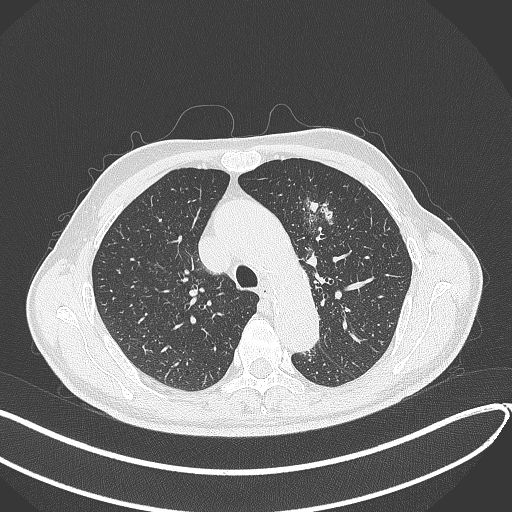
Chest CT, one axial slice. Reconstruction kernel B70f. 120 kVp. Lung window (W 1500 / L -600 HU). 512 × 512 image matrix, field of view 400 × 400 mm. Patient: male, 74 years. From the clinical record (not read from this slice): clinical TNM (as recorded): T2b N0 M1c.
Outlined on this slice (bounding box drawn by a radiologist):
- lung tumour (recorded histology: adenocarcinoma): bounding box (x1, y1, x2, y2) in pixels: (305, 196, 343, 246)